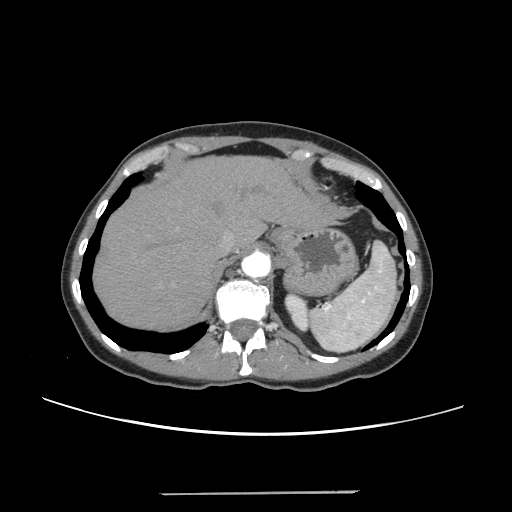
Contrast-enhanced abdominal CT, one axial slice. Slice 197 of 240 in the series (ordered by position). Intravenous contrast given. Soft-tissue window (W 400 / L 40 HU). 512 × 512 image matrix, field of view 371 × 371 mm. Female patient, age 60 years. From the clinical record (not read from this slice): diagnosis: colorectal cancer liver metastases, imaged before liver resection; multiple liver metastases: no; largest metastasis: 1.5 cm.
Outlined on this slice (manually delineated by an expert):
- hepatic veins: box from (x=221, y=232) to (x=234, y=251) px
- liver: (x=95, y=157)–(x=327, y=330)
- planned liver remnant (the part of the liver to remain after resection): (x=94, y=157)–(x=326, y=330)